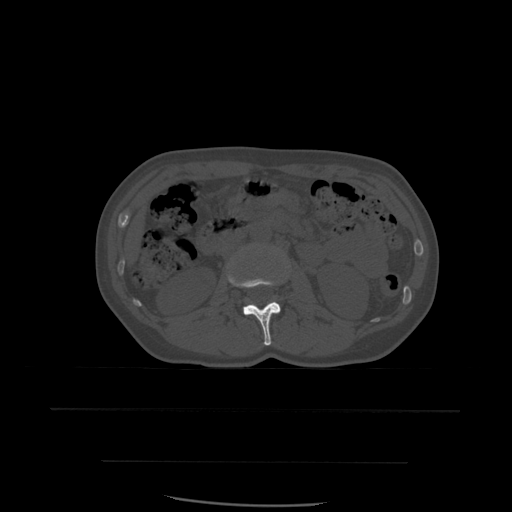
CT including the spine, one axial slice; position 217 of 574 along the scan axis; bone window (W 1800 / L 400 HU); 512 × 512 image matrix, field of view 392 × 392 mm. Patient age 48 years. Case-level facts recorded for this patient, not image findings: primary cancer: lung; vertebrae with lytic lesions (as recorded): T11.
Outlined on this slice (semi-automatically segmented with operator editing):
- L2 vertebra: bounding box (x1, y1, x2, y2) in pixels: (227, 271, 281, 346)